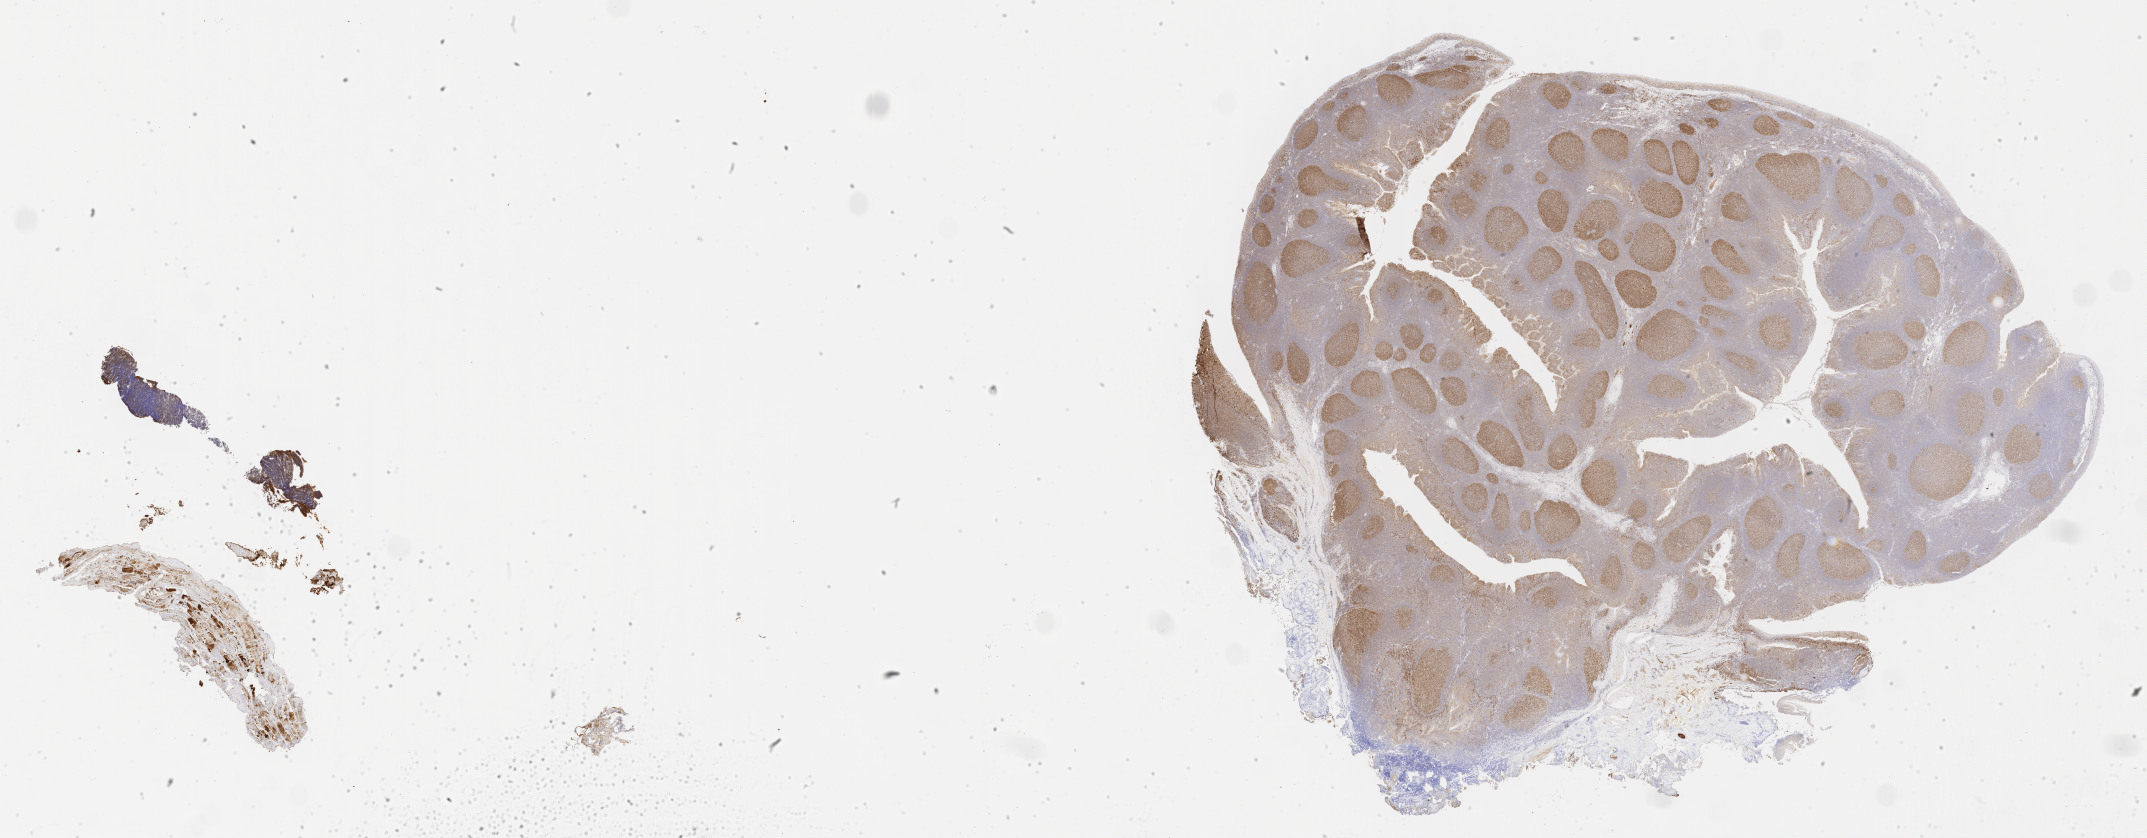
Immunohistochemistry (IHC) whole-slide image stained for BCL6, low-resolution overview of the scanned area, about 34.7 x 13.6 mm; specimen: tumor tissue; anatomic site: liver. Male patient.
* diagnosis: Burkitt lymphoma, NOS